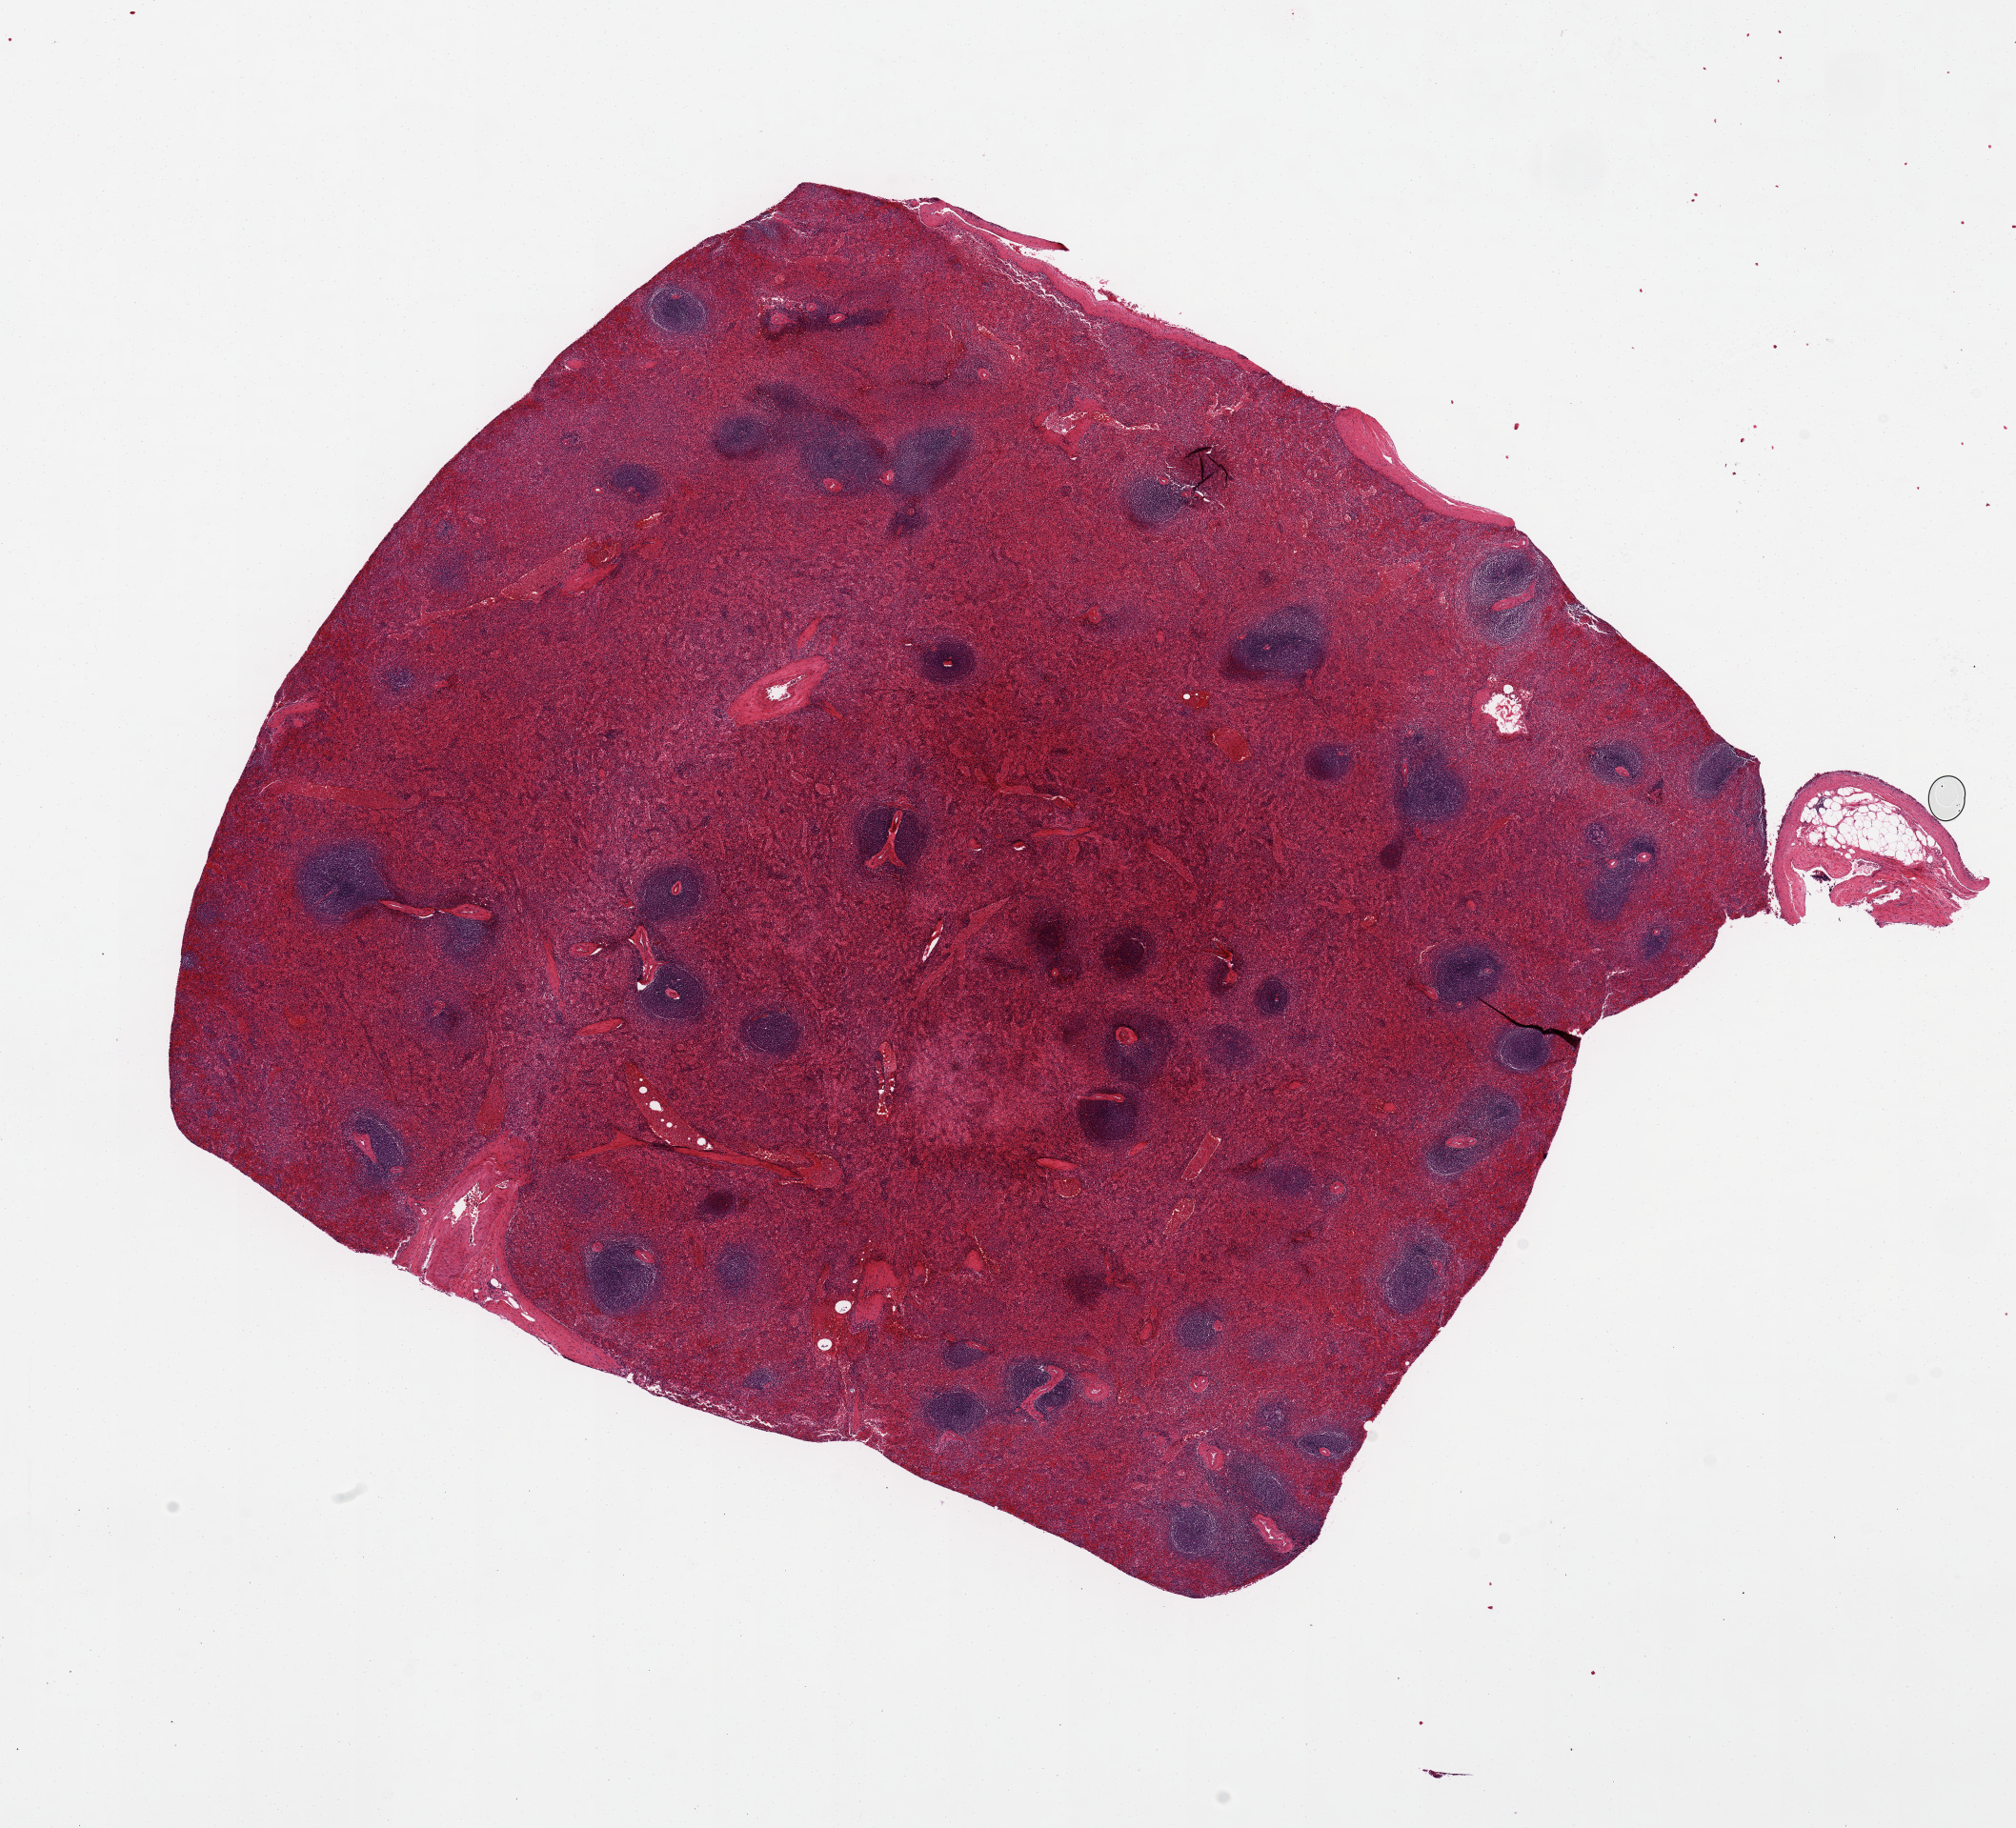
Digitized hematoxylin and eosin (H&E)-stained section, brightfield — whole scanned area (about 16.7 x 15.2 mm) shown as a low-resolution overview; PAXgene-fixed paraffin-embedded (PFPE) section; section of spleen (target tissue); donor tissue sample.
- review note (as recorded): Moderate congestion. 11x9.7mm